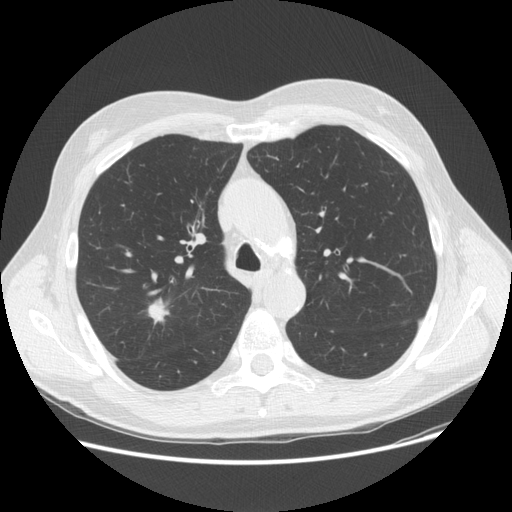
Low-dose screening chest CT, one axial slice. Slice 108 of 156 in the series (ordered by position). 120 kVp. Lung window (W 1500 / L -600 HU). 2.5 mm slice thickness. 512 × 512 image matrix, field of view 380 × 380 mm.
Outlined on this slice (manually delineated by an expert):
- lesion 1 (tumor, upper lobe of right lung): box from (x=148, y=298) to (x=170, y=325) px